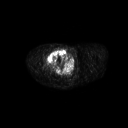
FDG PET of an extremity soft-tissue mass (from a PET/CT study), one axial slice; position 266 of 311 along the scan axis; 3.27 mm slice thickness; 128 × 128 image matrix, field of view 700 × 700 mm. Male patient, age 50 years. From the clinical record (not read from this slice): histological type: undifferentiated - pleiomorphic; grade: high; site of the primary tumour: right thigh.
Annotated regions visible in this slice (expert contour drawn on MRI and transferred to this co-registered scan by the dataset authors):
- gross tumour volume including surrounding oedema: bounding box [x1, y1, x2, y2] px = [45, 48, 67, 68]
- gross tumour volume (mass): [46, 48, 67, 68]